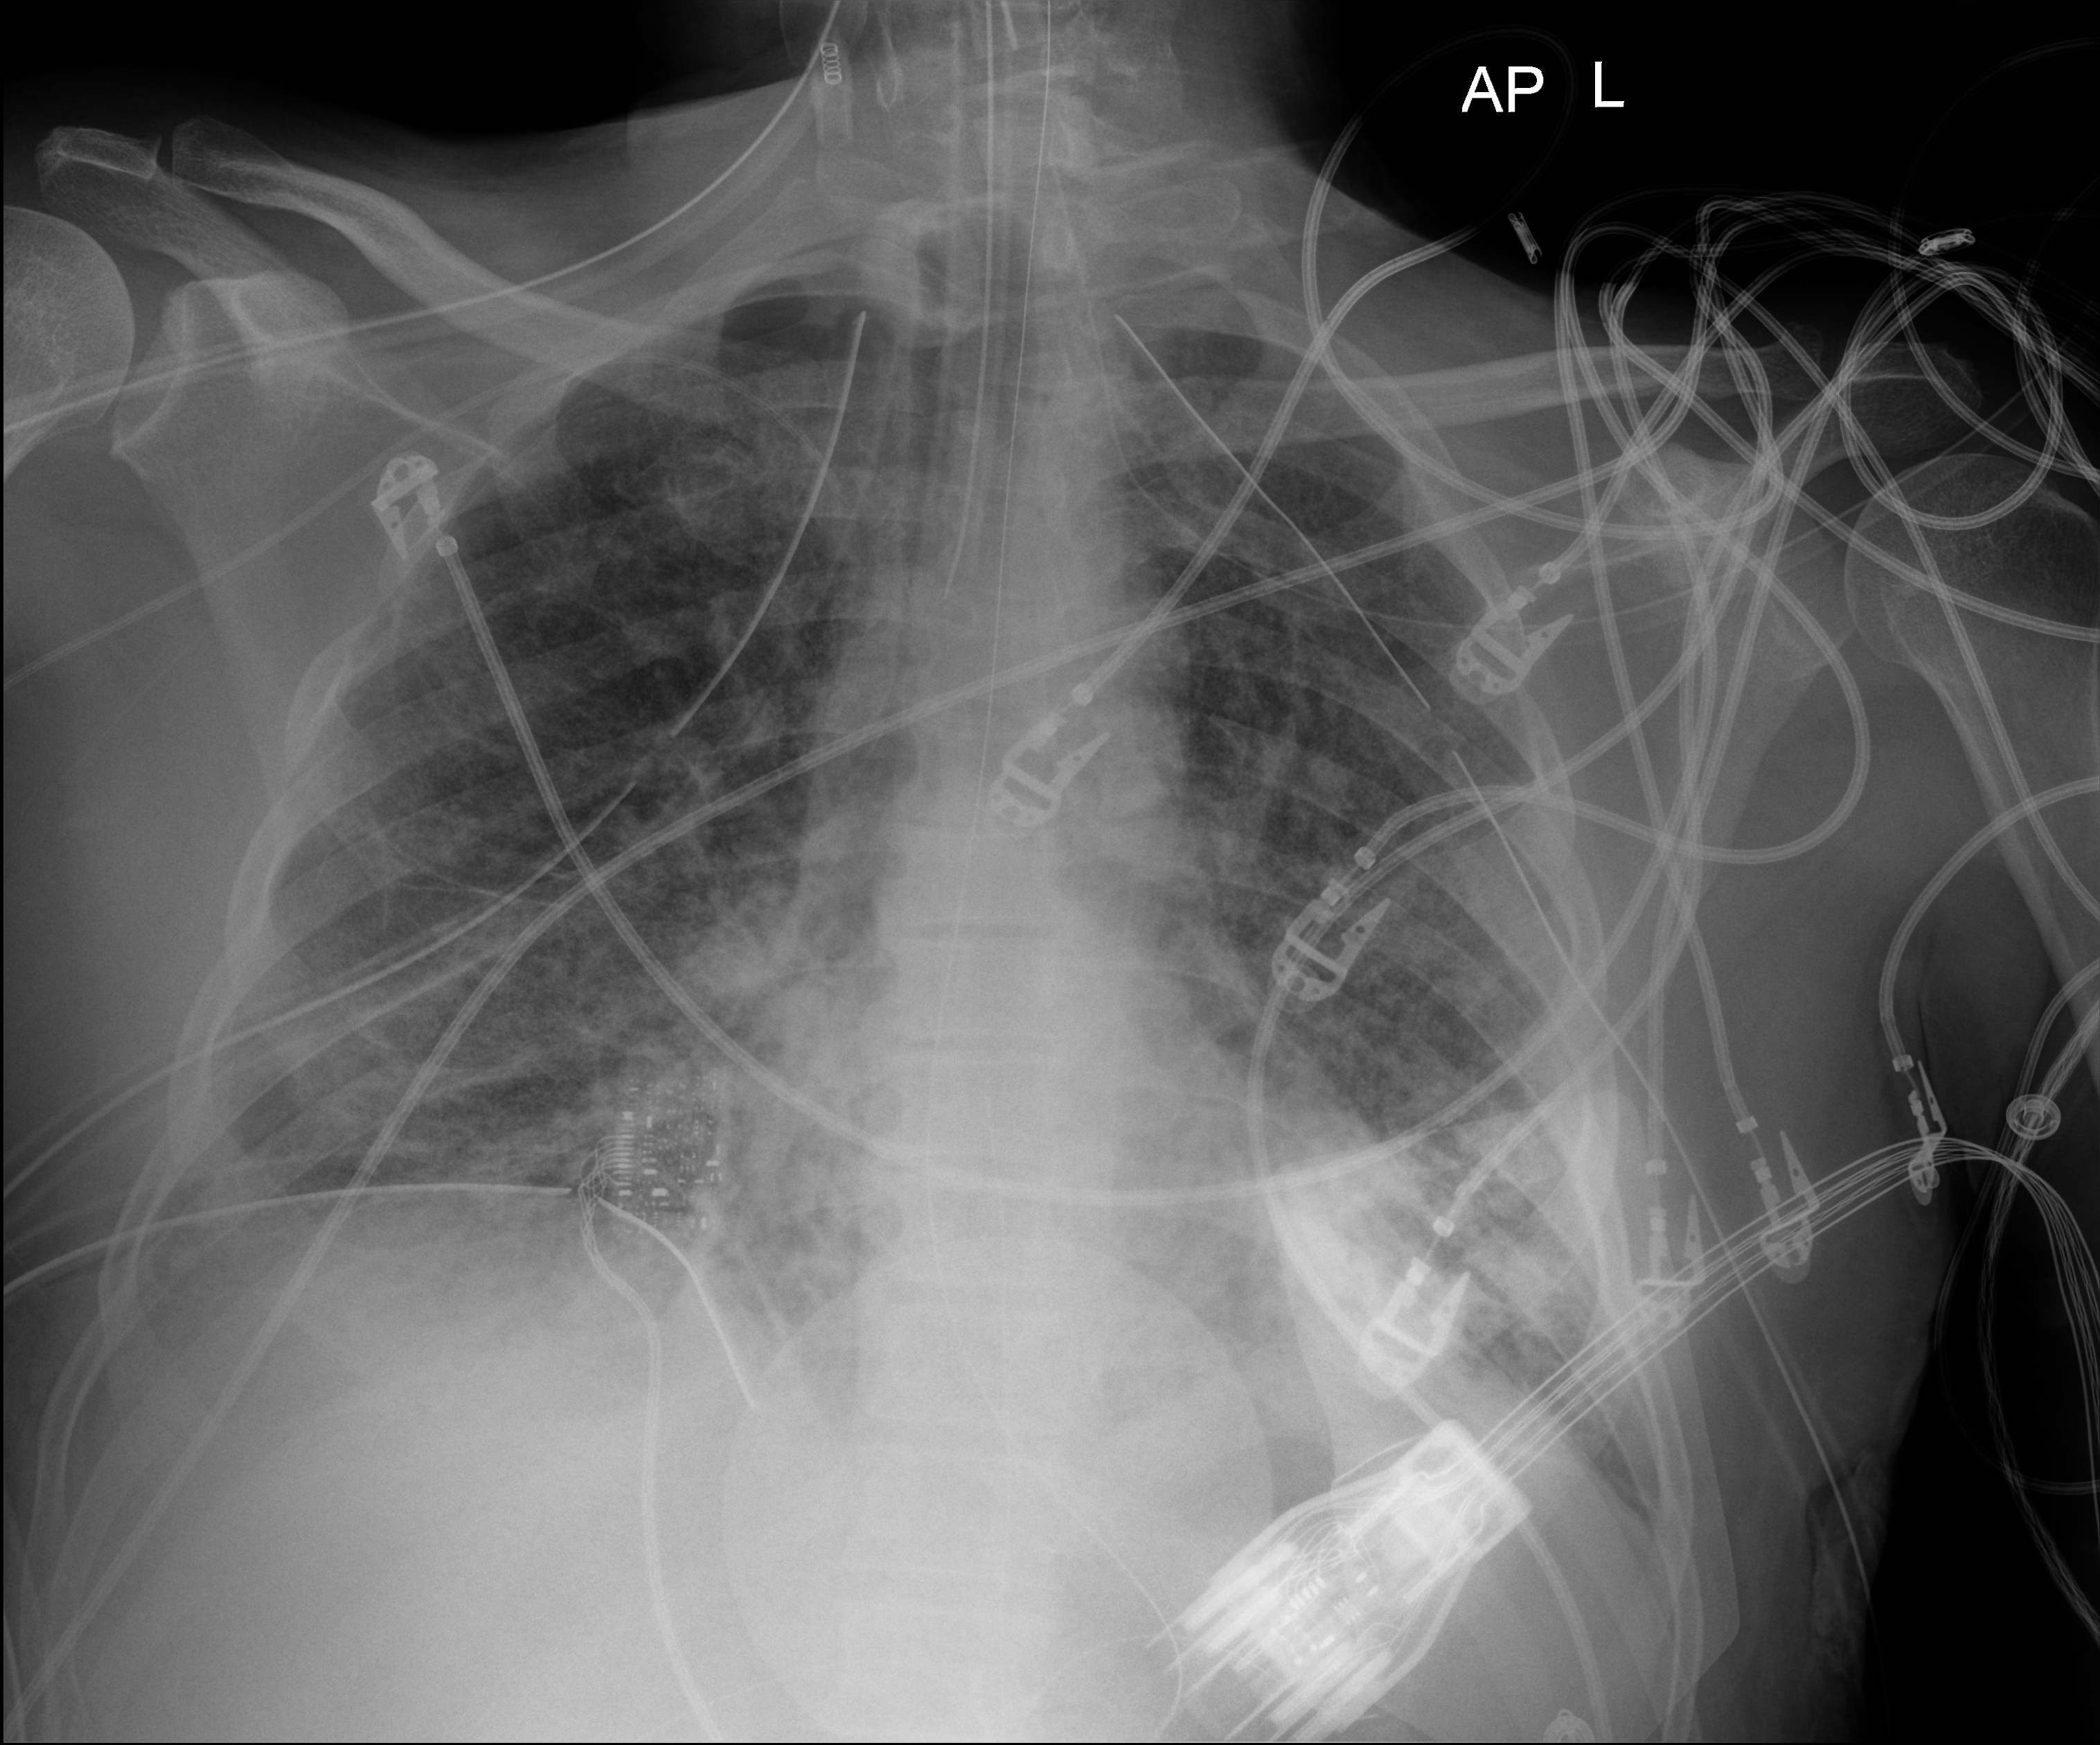
Portable chest radiograph. Patient hospitalised with COVID-19; male, aged 18–59 years.
Admission-level facts for this patient (not findings on this image; timing relative to this image not recorded): mechanically ventilated during this hospital stay: yes; admitted to intensive care during this hospital stay: yes.